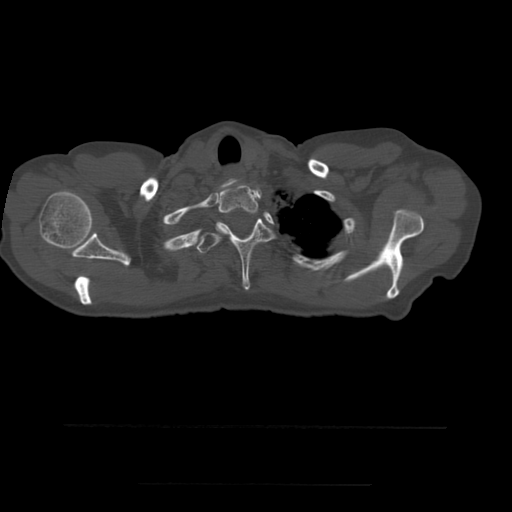
CT including the spine, one axial slice. Position 439 of 544 along the scan axis. Bone window (W 1800 / L 400 HU). 1.25 mm slice thickness. 512 × 512 image matrix, field of view 350 × 350 mm. Patient age 58 years. From the clinical record (not read from this slice): primary cancer: lung.
Structures marked on this image (semi-automatic segmentation, software-assisted and operator-edited):
- T1 vertebra: bounding box [x1, y1, x2, y2] px = [219, 184, 259, 214]
- T2 vertebra: [197, 218, 275, 290]